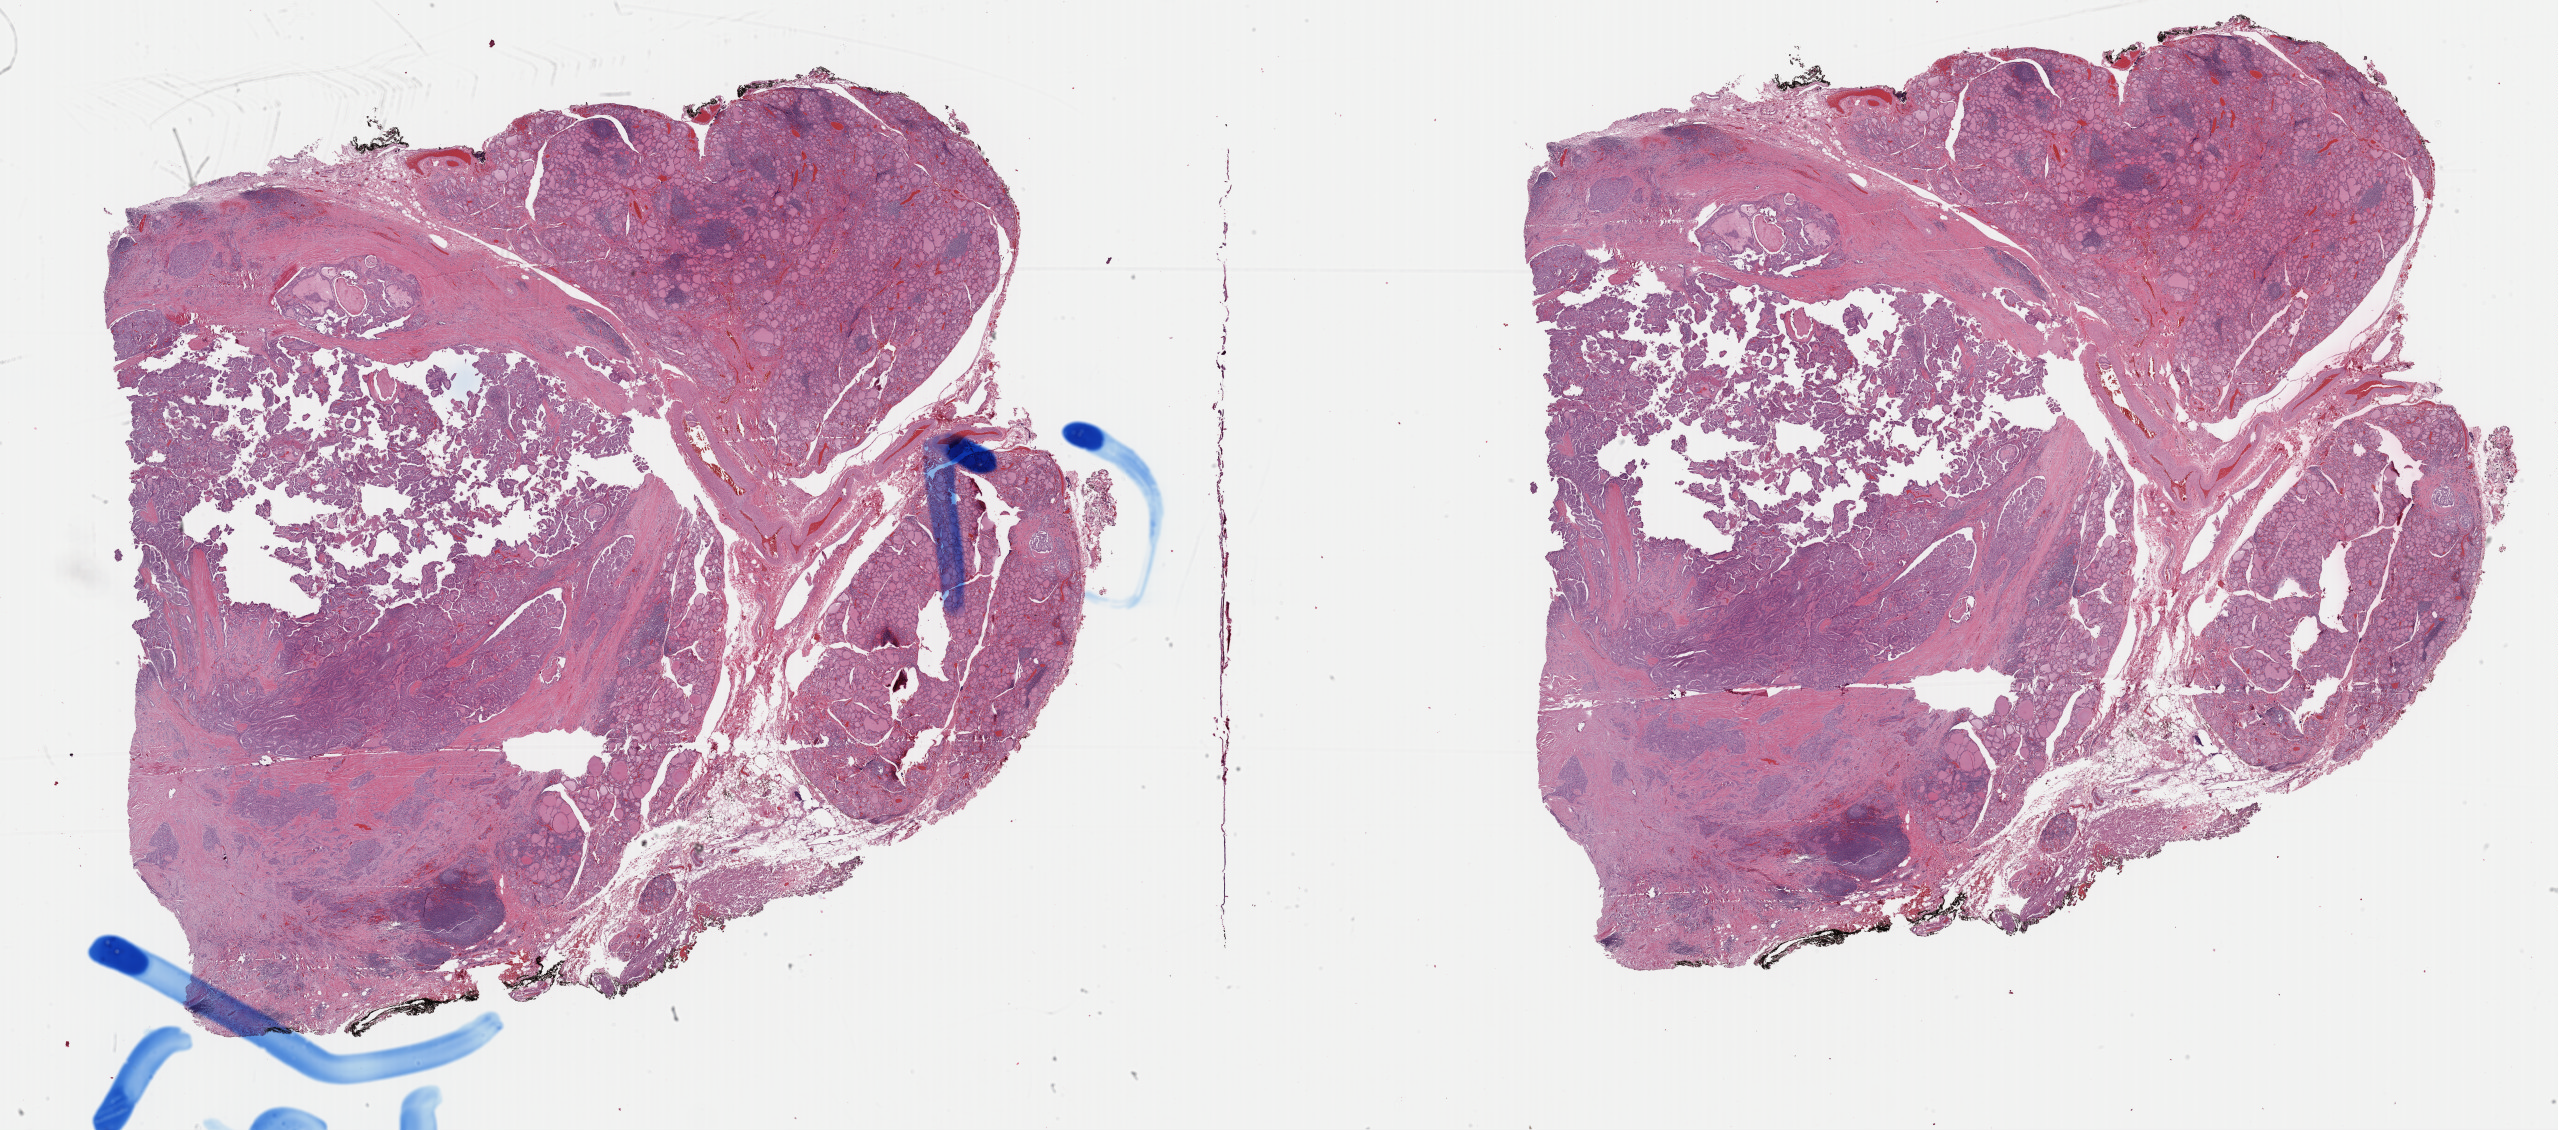
Whole-slide histology image, H&E-stained — whole scanned area (about 40.4 x 17.9 mm, slide scanned at 40x) shown as a low-resolution overview; formalin-fixed paraffin-embedded (FFPE) diagnostic section; primary tumour sample from the thyroid. Male, age 37 years at initial diagnosis.
* histologic diagnosis: Nonencapsulated sclerosing carcinoma (thyroid gland)
* laterality: right
* TNM: T3 N1b MX
* AJCC pathologic stage: I (7th edition)